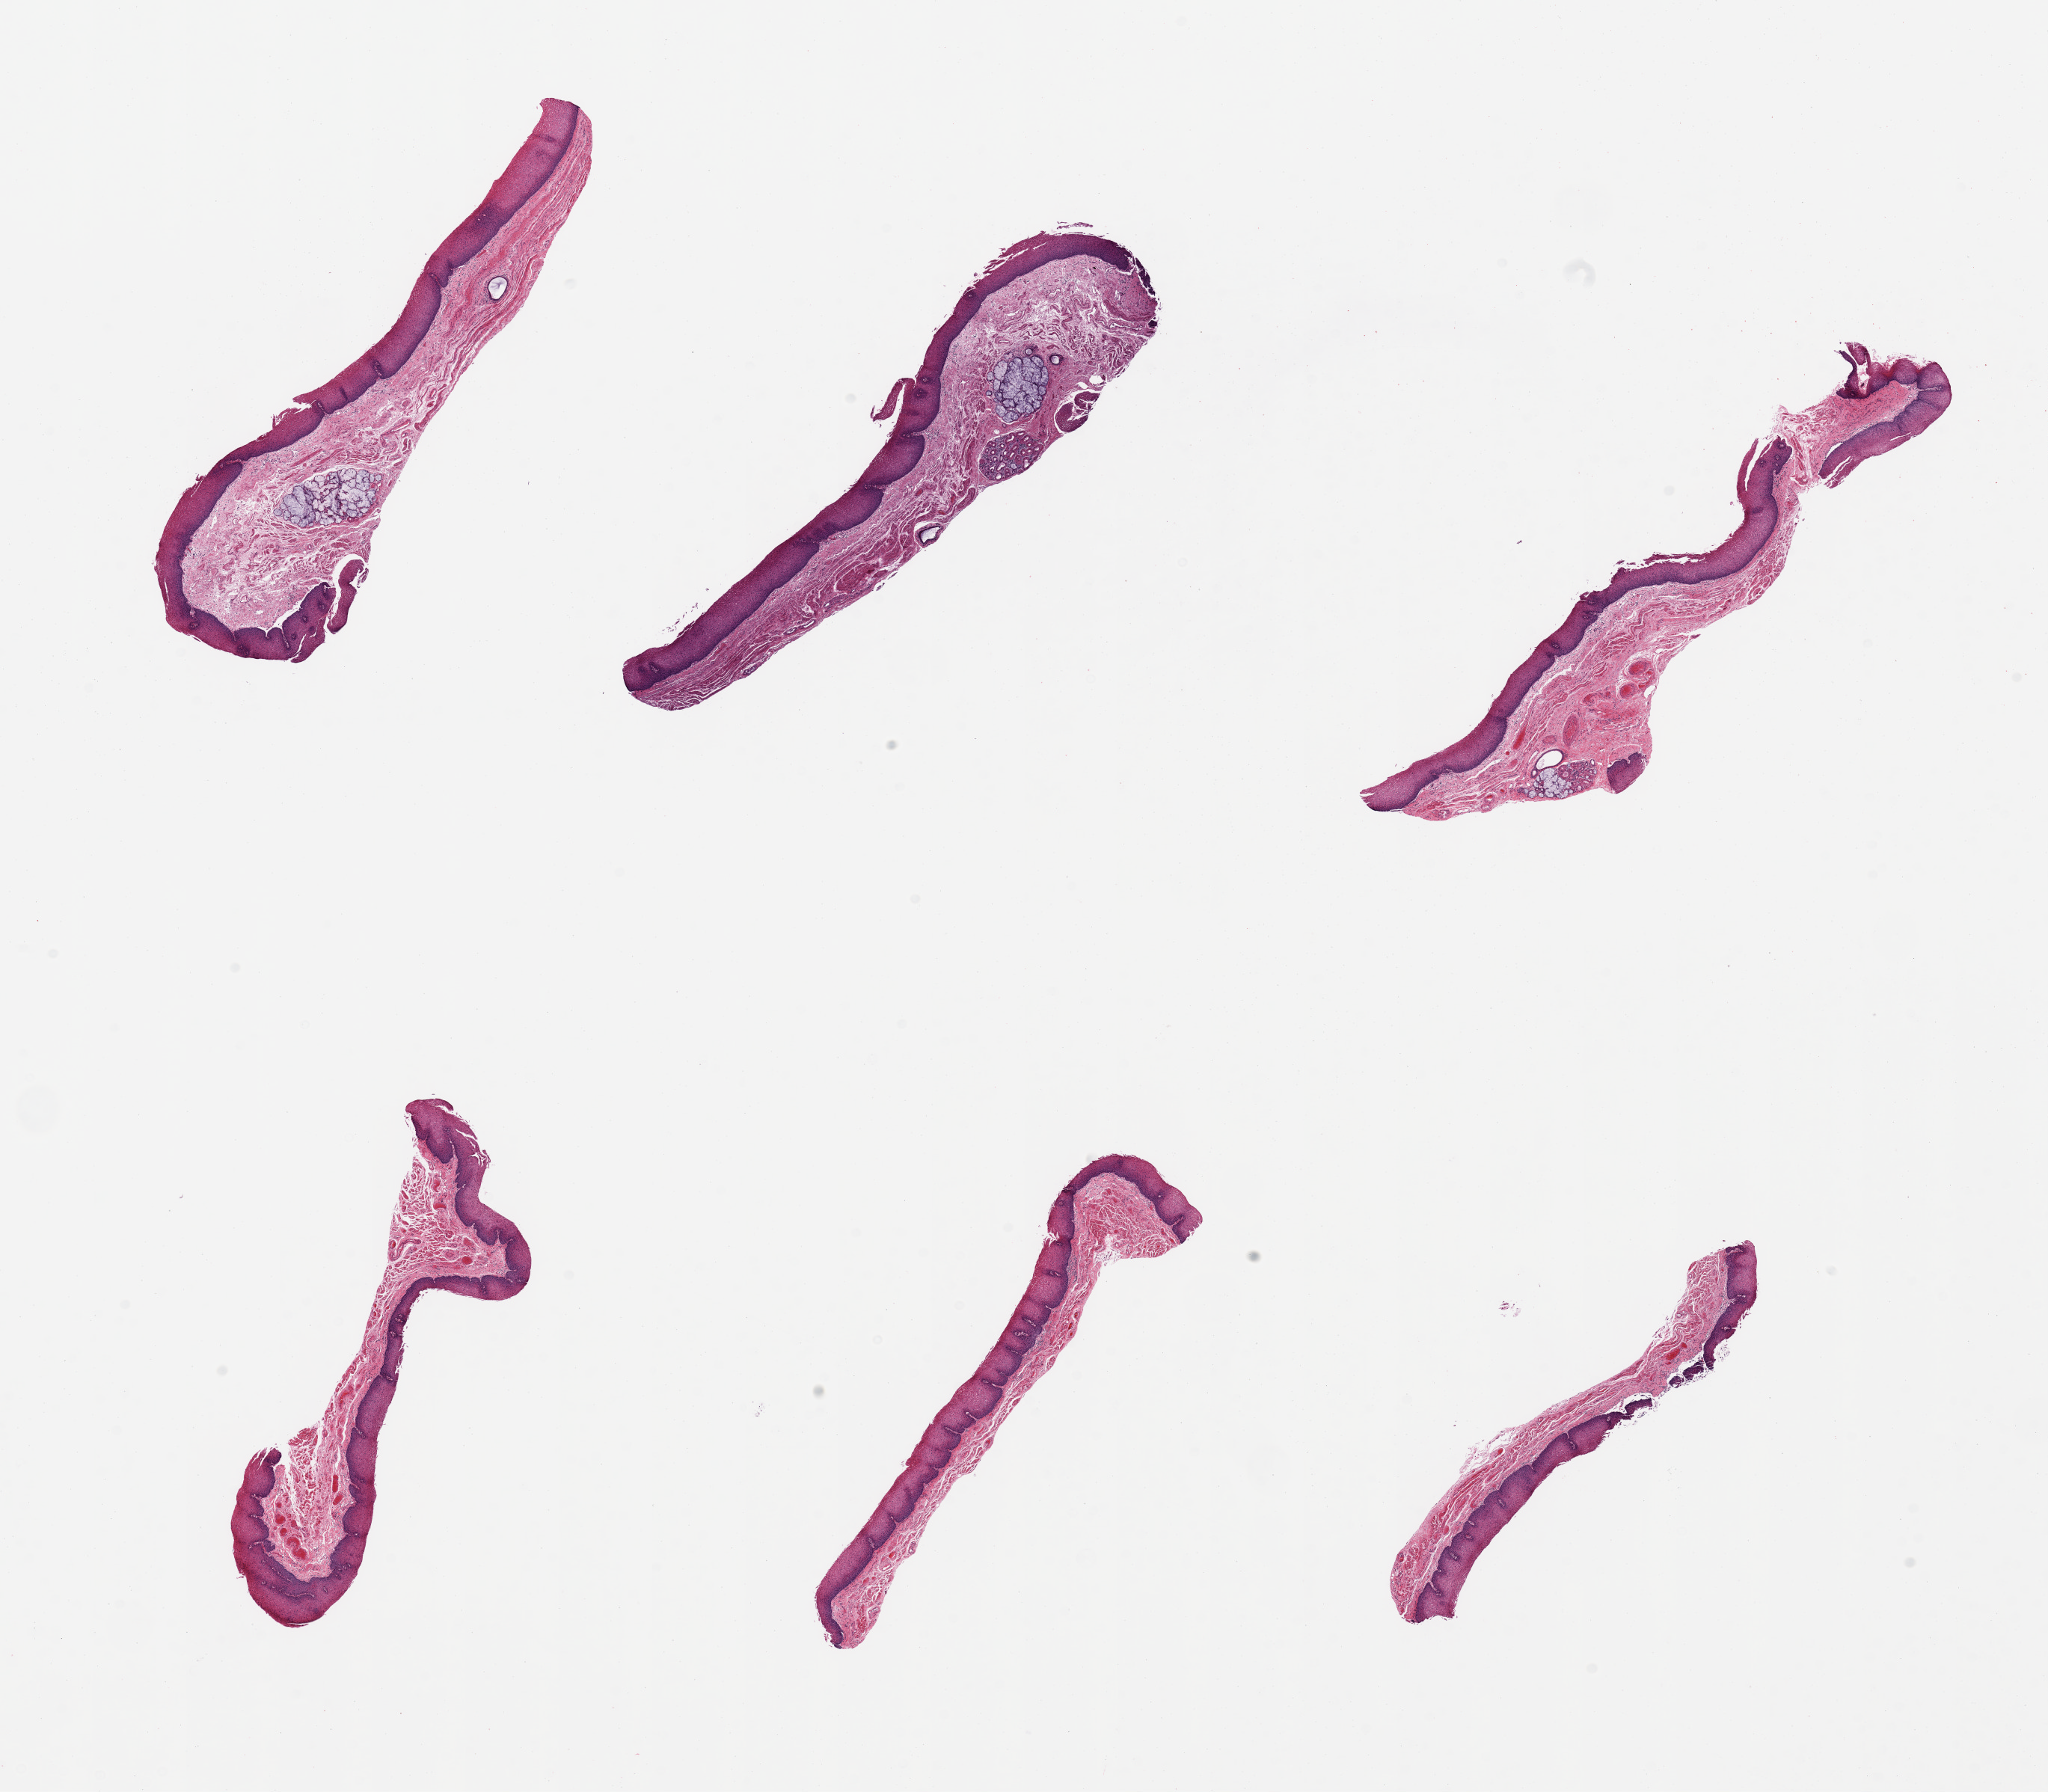
Digitized hematoxylin and eosin (H&E)-stained section, brightfield — a low-resolution overview of the entire scanned area, about 21.7 x 19.0 mm (from a 20x scan), PAXgene-fixed, paraffin-embedded tissue, section of esophageal mucous membrane (target tissue), donor tissue sample. Donor sex: male.
• reviewer comment on this tissue sample: 6 pieces, squamous mucosa ~20% thickness, prominent submucosal glands noted